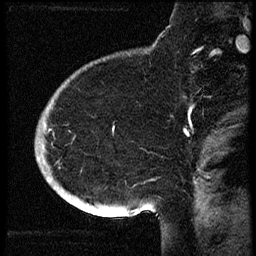
Breast MRI (dynamic contrast-enhanced), one sagittal slice; dynamic contrast-enhanced study with each time point stored as its own series, time point 2 of 3 at this slice position (early post-contrast, ordered by acquisition time); 1.5 T; TE 4.2 ms, TR 18.9 ms; 2 mm slice thickness; 256 × 256 image matrix. Female patient. Case-level facts recorded for this patient, not image findings: setting: breast cancer imaged before/during neoadjuvant chemotherapy; receptor status: HR-positive, HER2-negative.
Structures marked on this image (semi-automatic segmentation, software-assisted and operator-edited):
- analysis volume of interest (the breast-tissue region the enhancement analysis was run in; not a lesion): bounding box <38,87,104,173> (left, top, right, bottom; pixels)
- tumour enhancement mask (voxels above the 100 % enhancement threshold inside the analysis volume of interest): <44,125,46,127>